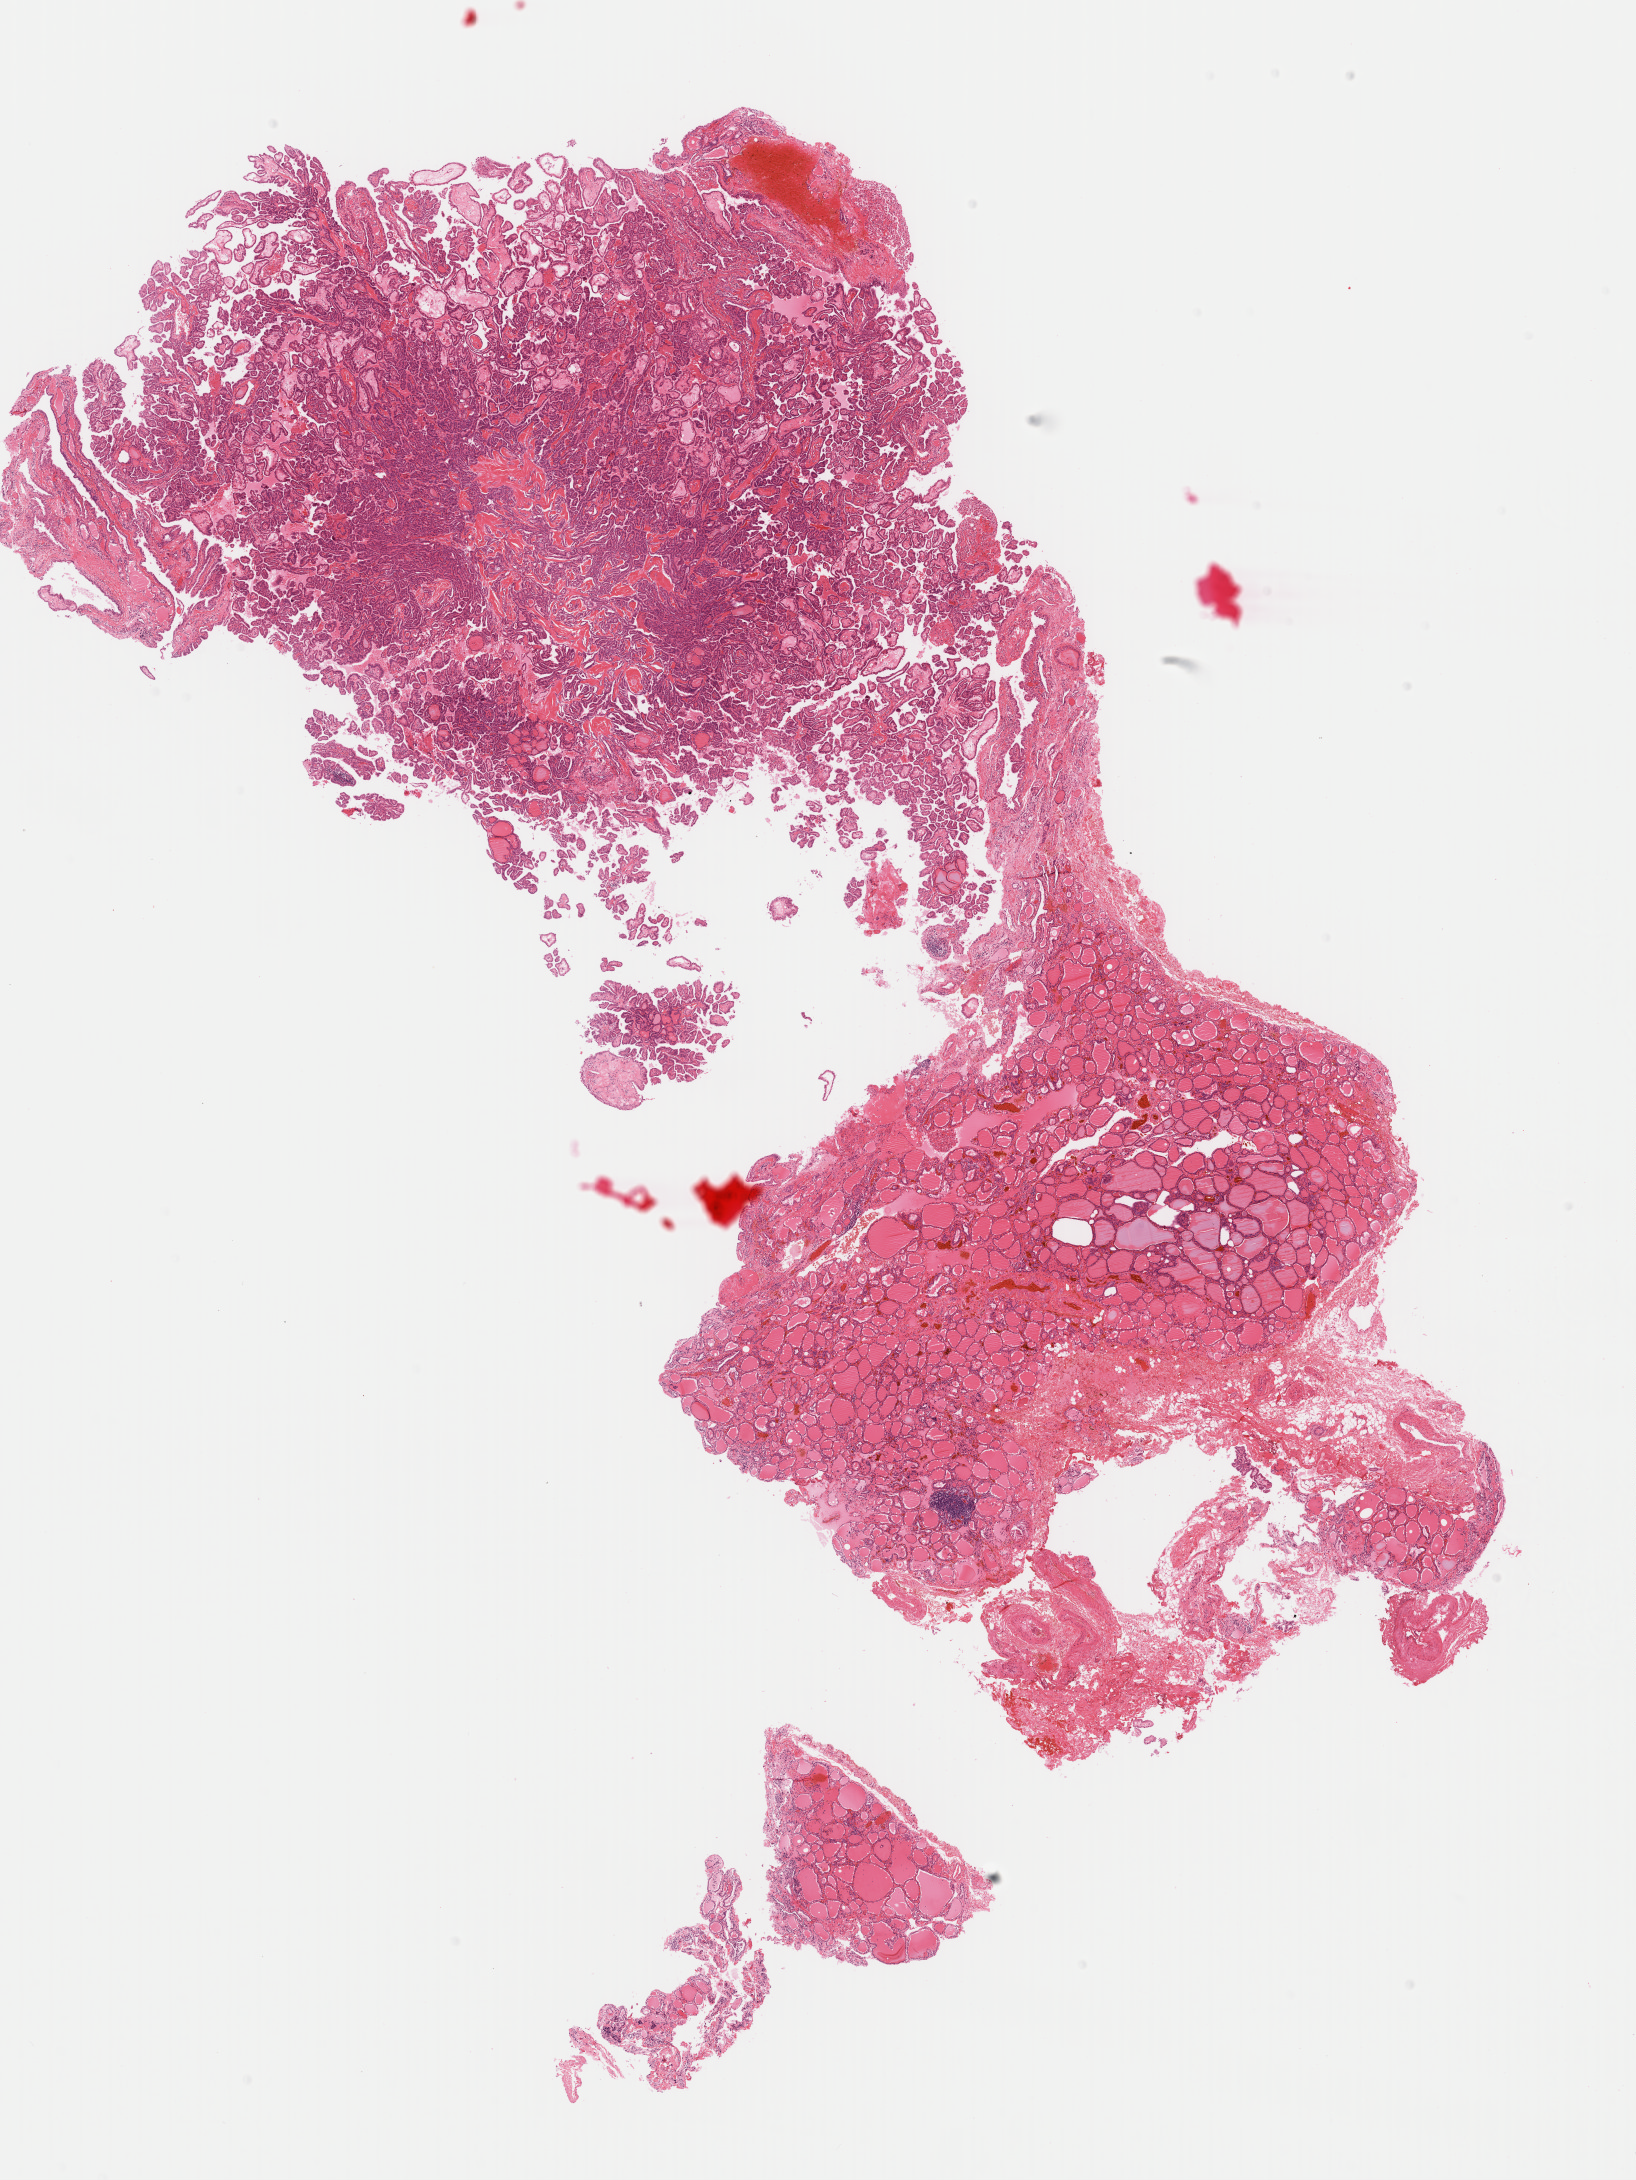
H&E-stained whole-slide image — shown as a low-resolution overview of the whole scanned area (about 12.9 x 17.2 mm, from a 40x scan); FFPE section; primary tumour sample from the thyroid. Female, age 39 years at initial diagnosis.
AJCC pathologic stage: I (7th edition). Lymph nodes positive (case pathology): 1 of 2 examined. TNM: T1a N1b M0. Histologic diagnosis: Papillary adenocarcinoma, NOS (thyroid gland).